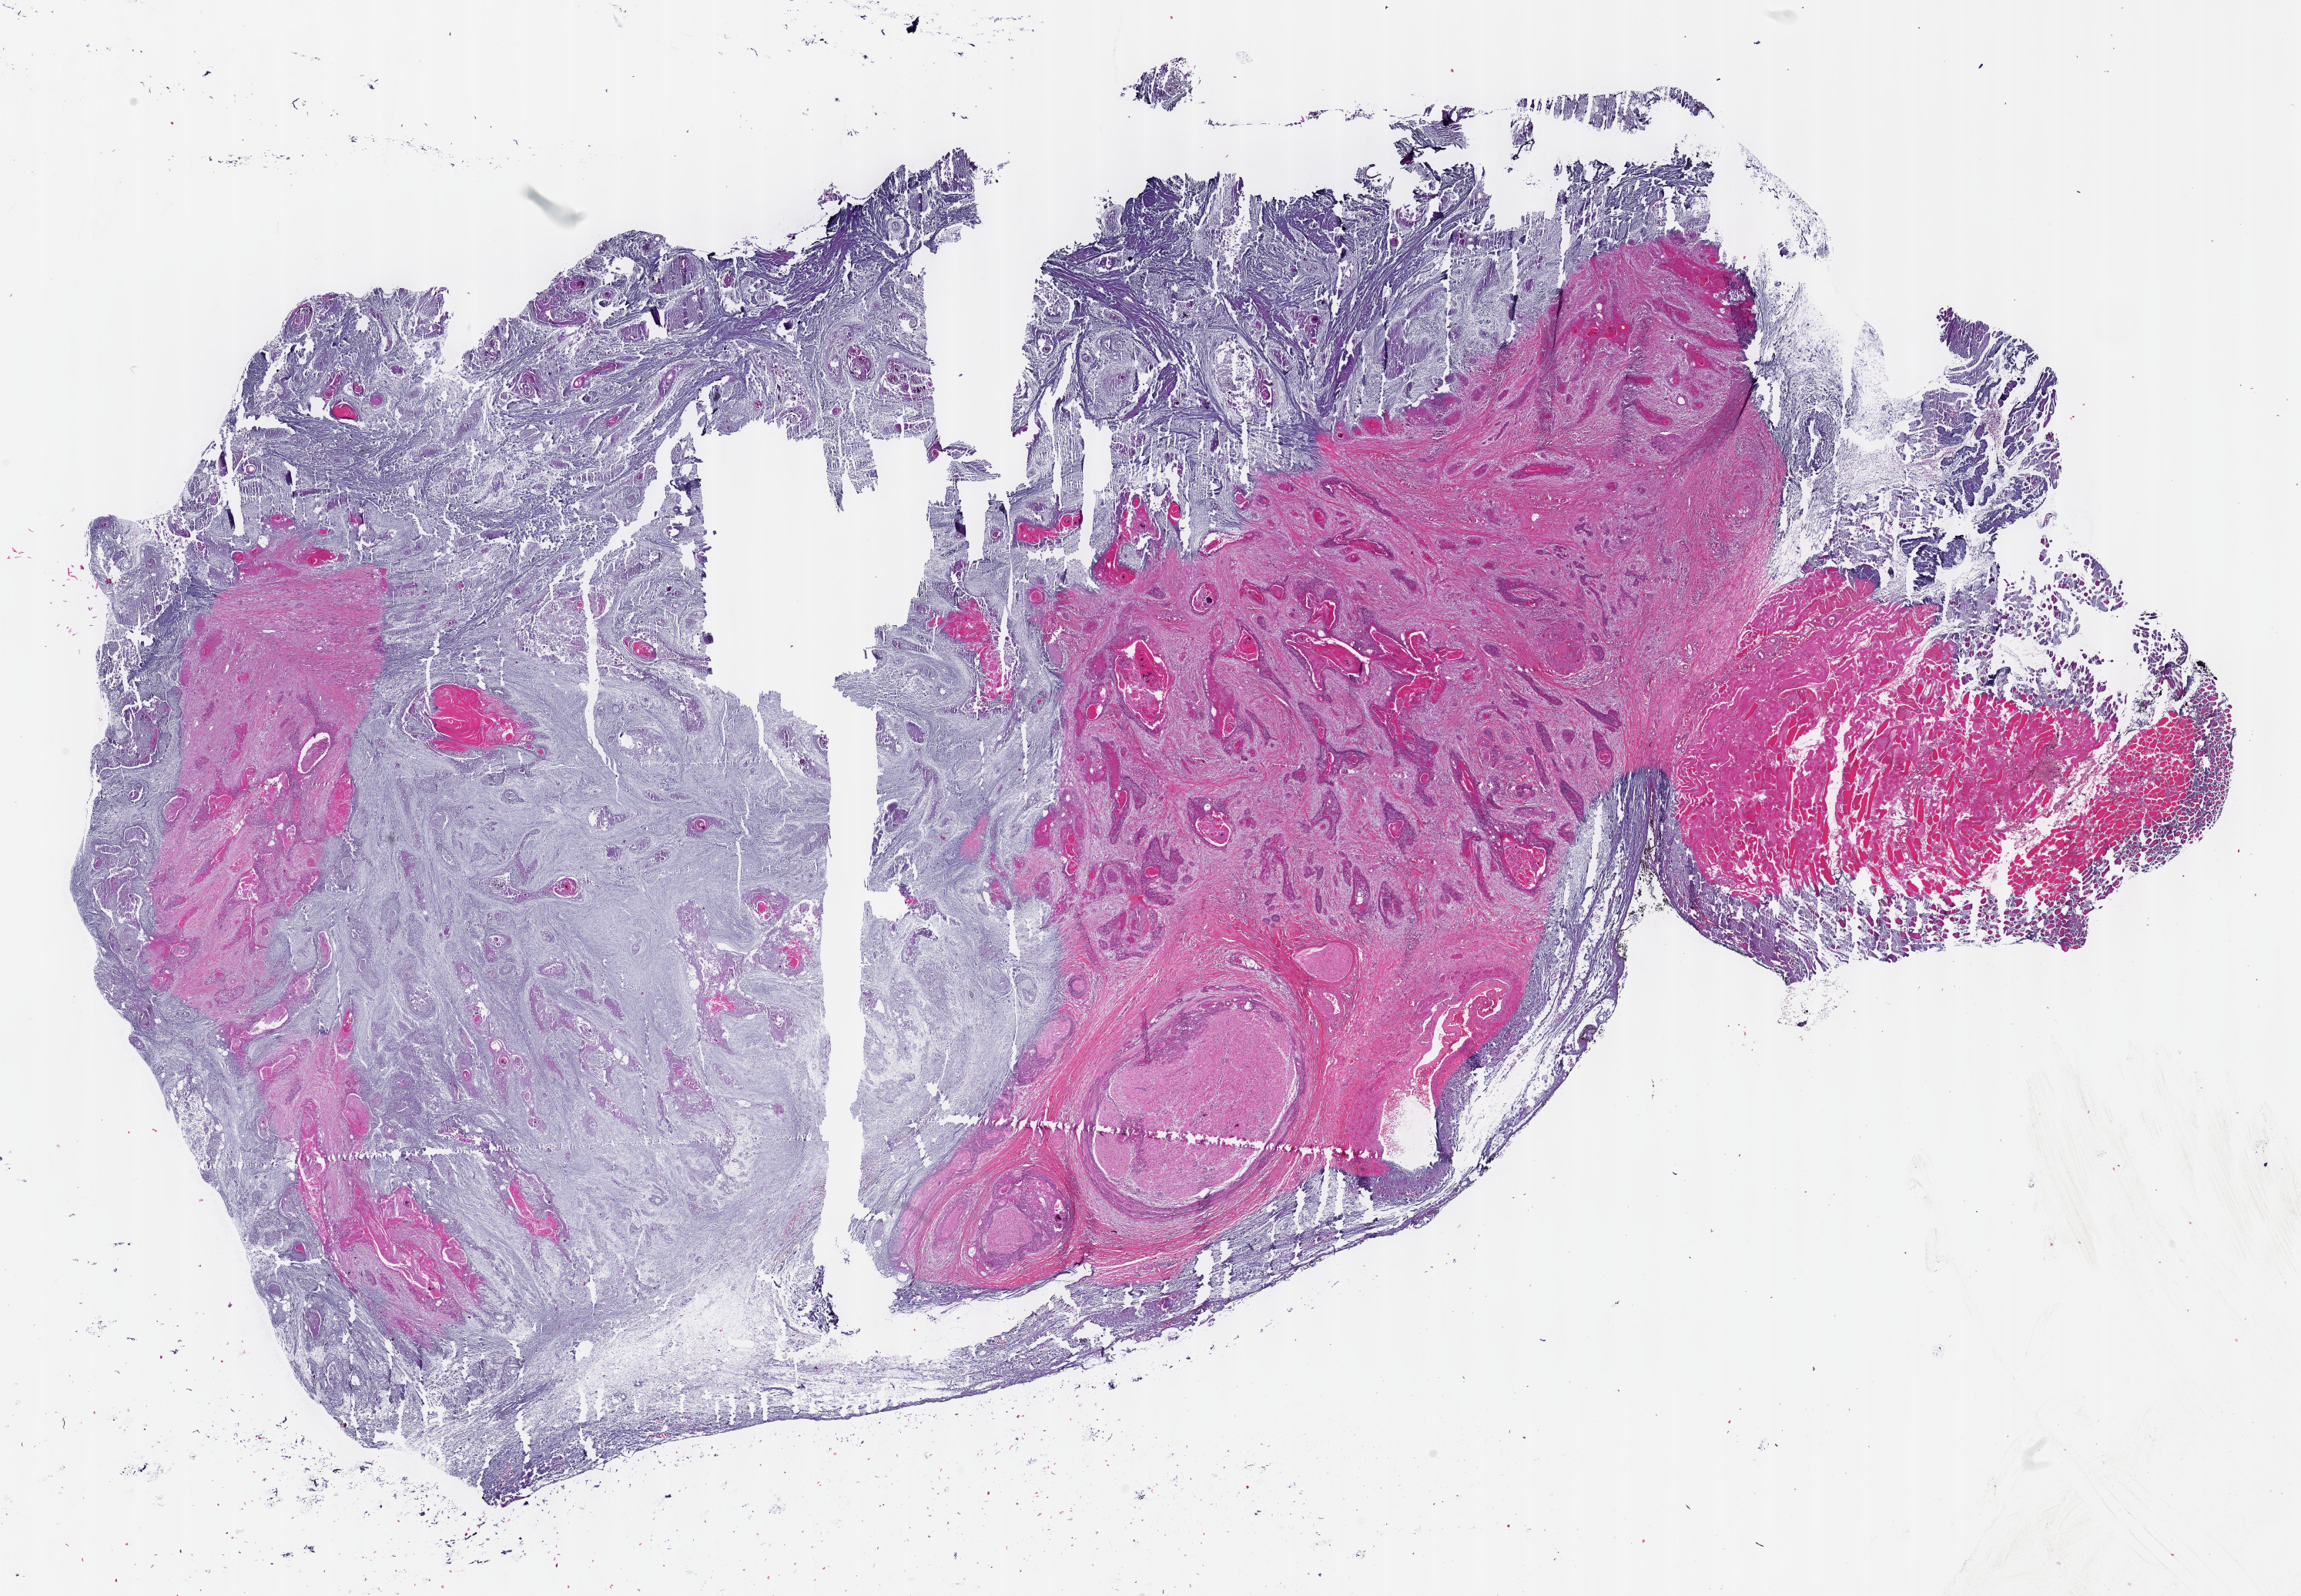
Digitized Hematoxylin and eosin (H&E) stained tissue section (whole slide), whole scanned area (about 24.1 x 16.7 mm) shown as a low-resolution overview. Formalin-fixed paraffin-embedded (FFPE) diagnostic section. Head and neck, primary tumour sample. Female patient; age at initial diagnosis 66 years. Histologic grade: G2 (moderately differentiated).
- TNM: T3 N2b
- AJCC pathologic stage: IVA (7th edition)
- diagnosis: Squamous cell carcinoma, NOS (tongue, NOS)